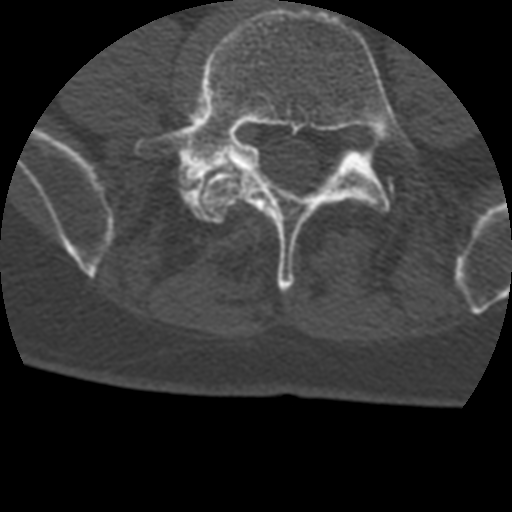
CT including the spine, one axial slice. Slice 46 of 399 in the series (ordered by position). Reconstruction kernel STANDARD. Bone window (W 1800 / L 400 HU). 1.25 mm slice thickness. 512 × 512 image matrix. Patient age 69 years. Case-level facts recorded for this patient, not image findings: primary cancer: prostate.
Structures marked on this image (semi-automatic segmentation, software-assisted and operator-edited):
- L4 vertebra: box from (x=198, y=171) to (x=245, y=221) px
- L5 vertebra: (x=135, y=7)–(x=417, y=292)